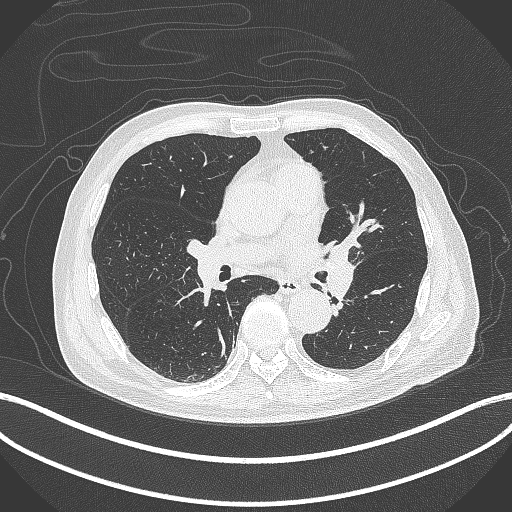
Chest CT, one axial slice. Position 226 of 417 along the scan axis. 120 kVp. Lung window (W 1500 / L -600 HU). 1 mm slice thickness. 512 × 512 image matrix, field of view 400 × 400 mm. Male patient, age 77 years. Case-level facts recorded for this patient, not image findings: clinical TNM (as recorded): T3 N1 M0.
Outlined on this slice (rectangle marked by the reading radiologist):
- lung tumour (recorded histology: adenocarcinoma): bounding box (x1, y1, x2, y2) in pixels: (322, 240, 358, 304)